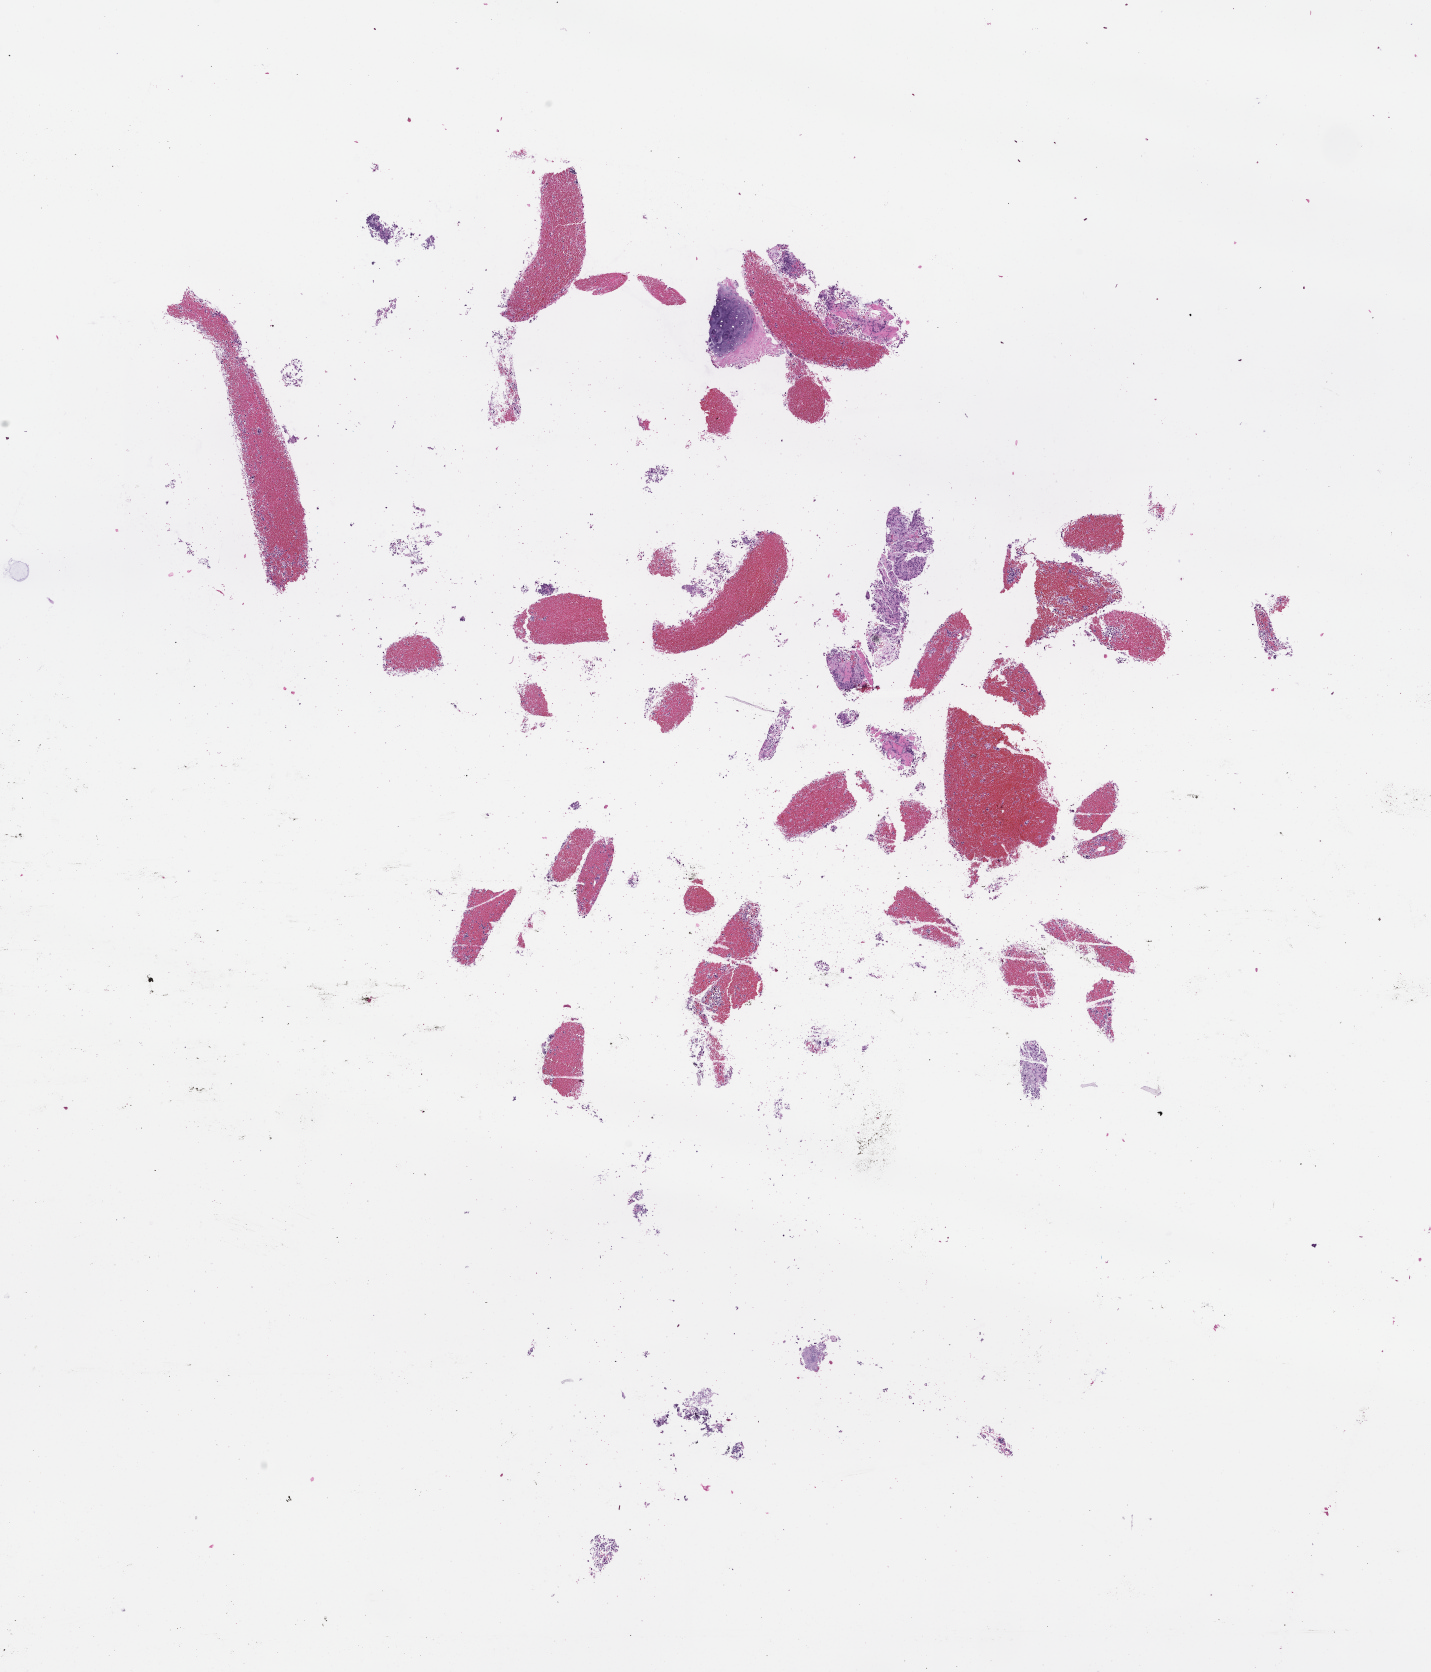
Whole-slide image, haematoxylin and eosin stain, shown as a low-resolution overview of the whole scanned area (about 11.6 x 13.5 mm). Formalin-fixed paraffin-embedded section. Specimen time point: archival tissue. Patient sex: male.
This section: metastatic tumor tissue. Patient diagnosis (primary): Non-Small Cell Lung Carcinoma.